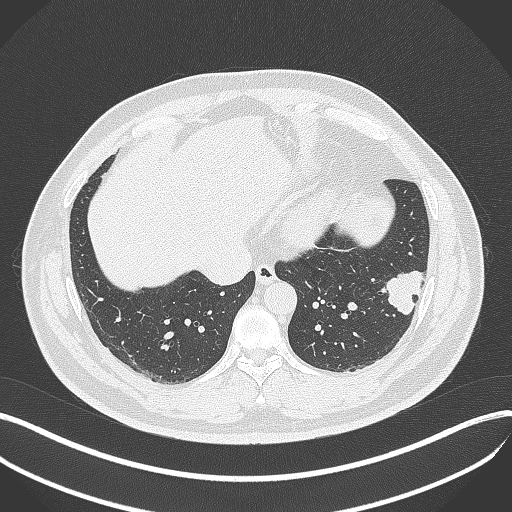
Chest CT, one axial slice; position 126 of 429 along the scan axis; lung window (W 1500 / L -600 HU); 512 × 512 image matrix. Male patient, age 39 years. From the clinical record (not read from this slice): clinical TNM (as recorded): T2a N0 M0.
Outlined on this slice (rectangle marked by the reading radiologist):
- lung tumour (recorded histology: adenocarcinoma): bounding box (x1, y1, x2, y2) in pixels: (377, 263, 433, 321)